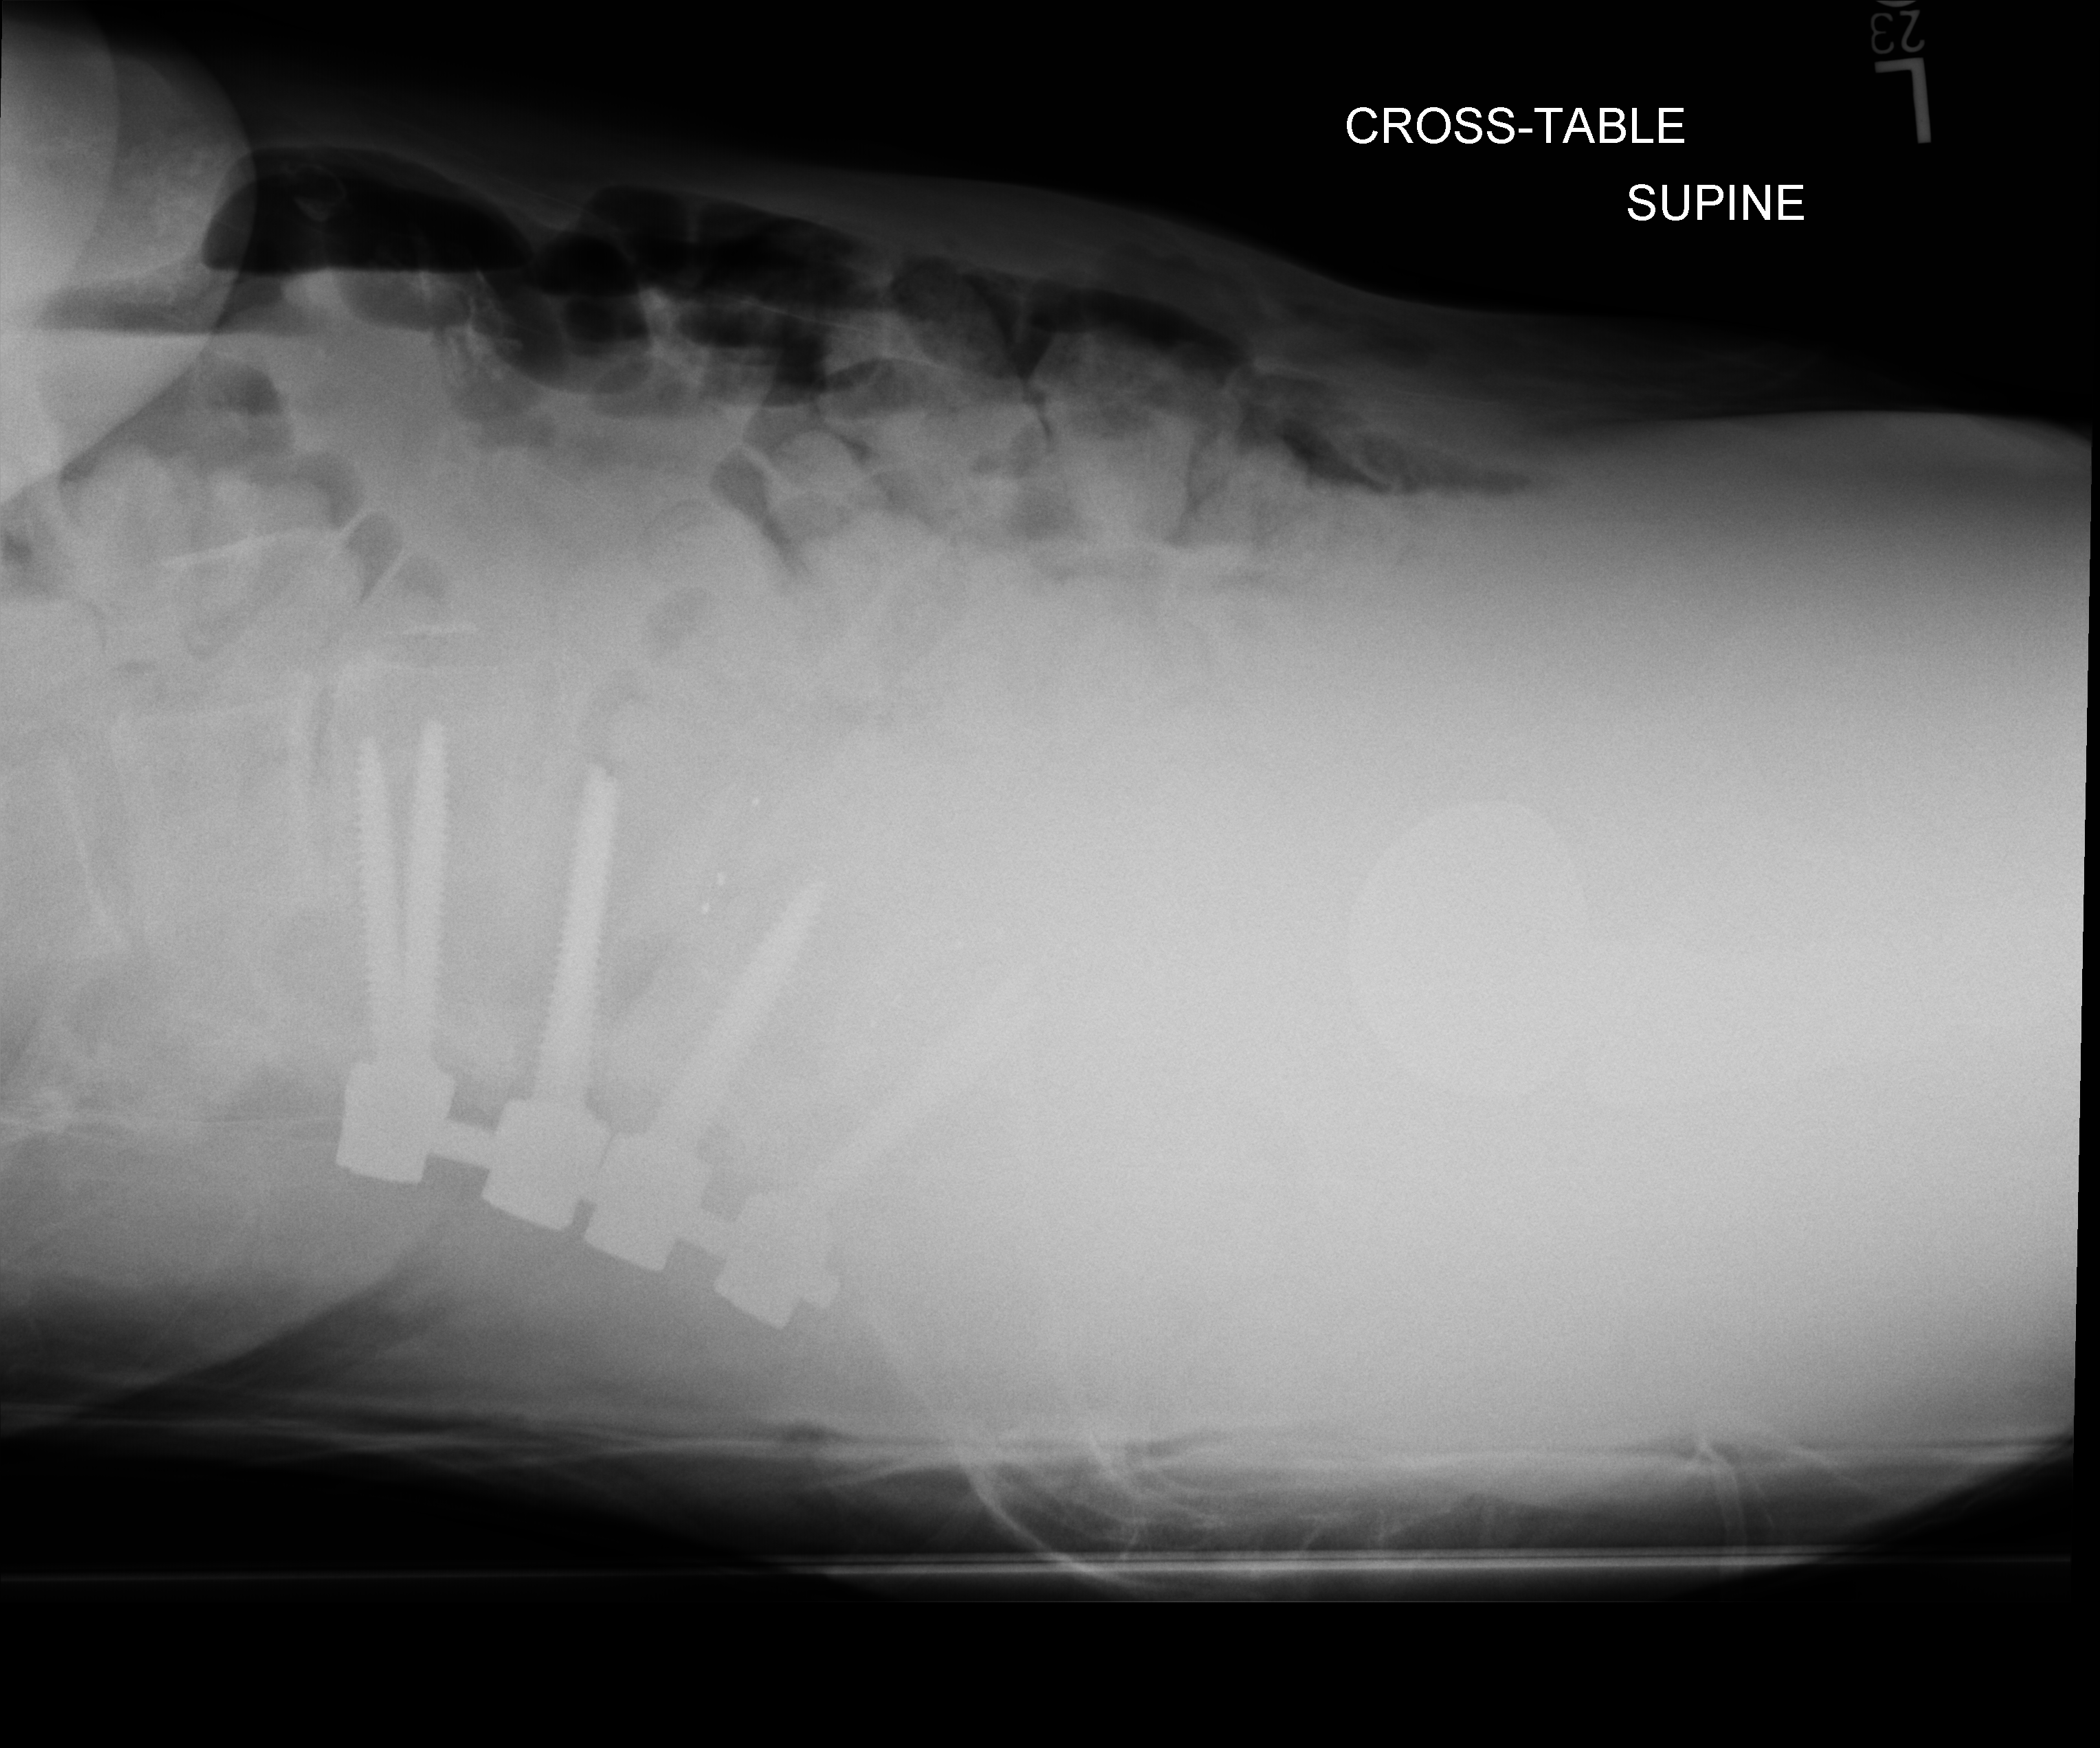
Abdomen X-ray. Patient hospitalised with COVID-19; female, aged 60–74 years.
From the hospital-stay record, not from the radiograph (when in the stay this image was taken is not recorded):
- mechanically ventilated during this hospital stay: no
- admitted to intensive care during this hospital stay: no